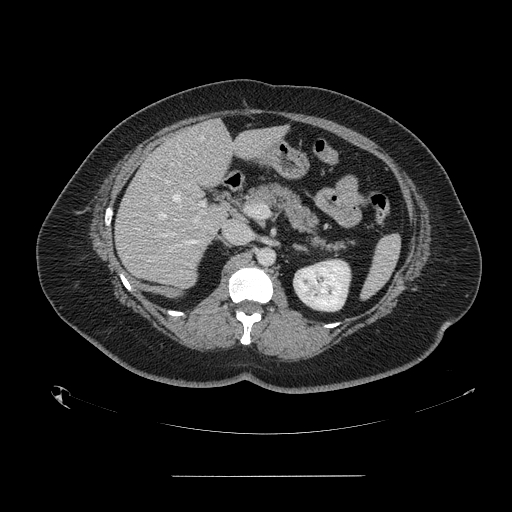
Contrast-enhanced abdominal CT, one axial slice. Slice 82 of 164 in the series (ordered by position). 120 kVp. Soft-tissue window (W 400 / L 40 HU). 2.5 mm slice thickness. 512 × 512 image matrix, field of view 495 × 495 mm. Female patient, age 52 years. Case-level facts recorded for this patient, not image findings: diagnosis: colorectal cancer liver metastases, imaged before liver resection; multiple liver metastases: yes; largest metastasis: 3.5 cm; disease in both lobes: no.
Annotated regions visible in this slice (outlined manually by an expert reader):
- hepatic veins: box from (x=153, y=136) to (x=203, y=218) px
- liver: (x=116, y=121)–(x=283, y=288)
- planned liver remnant (the part of the liver to remain after resection): (x=177, y=121)–(x=283, y=186)
- portal vein (with intrahepatic branches): (x=160, y=179)–(x=205, y=237)